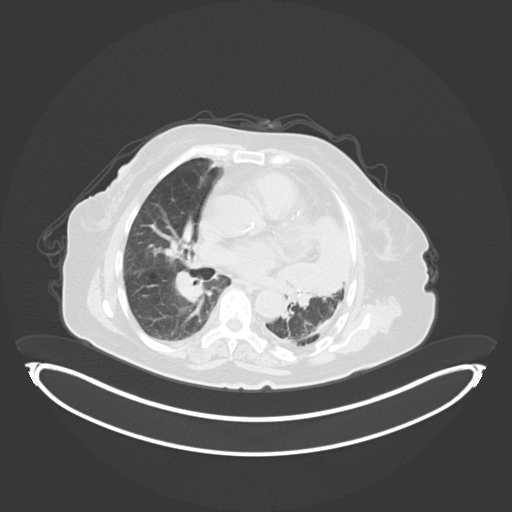
Chest CT, one axial slice. Position 194 of 284 along the scan axis. Reconstruction kernel B30f. 120 kVp. Lung window (W 1500 / L -600 HU). 3 mm slice thickness. 512 × 512 image matrix, field of view 500 × 500 mm. Patient: female, 75 years. From the clinical record (not read from this slice): clinical TNM (as recorded): T3 N3 M1.
Structures marked on this image (bounding box drawn by a radiologist):
- lung tumour (recorded histology: adenocarcinoma): bounding box <278,209,354,301> (left, top, right, bottom; pixels)